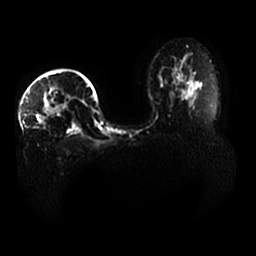
Breast MRI, one axial slice; slice 27 of 33 in the series (ordered by position); diffusion-weighted series; image 2 of 4 stored at this slice position (different b-values; order by instance number); 1.5 T; 256 × 256 image matrix. Female patient.
Annotated regions visible in this slice (outlined manually by an expert reader):
- tumour on diffusion-weighted imaging: bounding box [x1, y1, x2, y2] px = [41, 96, 82, 125]